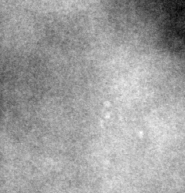
Crop from a digitized film mammogram around one marked abnormality; right breast; CC view.
Calcifications, morphology pleomorphic, distribution clustered; BI-RADS assessment category 4; pathology result (as recorded, not read from the image): benign.